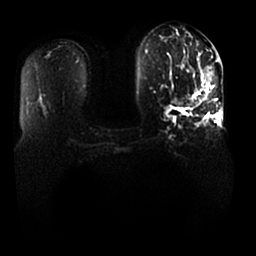
Breast MRI, one axial slice; position 9 of 25 along the scan axis; diffusion-weighted series; image 2 of 4 stored at this slice position (different b-values; order by instance number); 1.5 T; 4 mm slice thickness; 256 × 256 image matrix, field of view 370 × 370 mm. Female patient.
Outlined on this slice (expert manual segmentation):
- tumour on diffusion-weighted imaging: bounding box <173,71,211,105> (left, top, right, bottom; pixels)